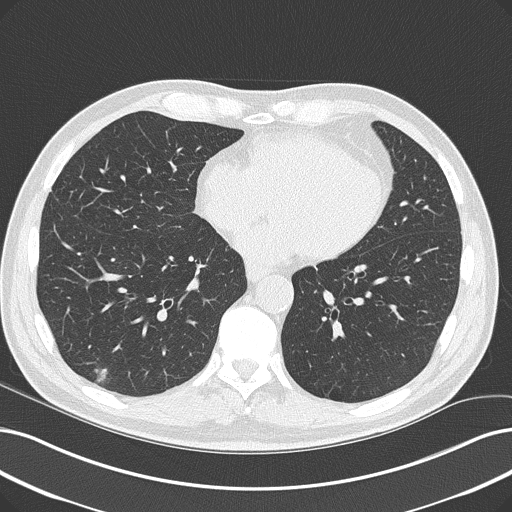
Low-dose screening chest CT, one axial slice. Slice 89 of 228 in the series (ordered by position). Reconstruction kernel B50f. Lung window (W 1500 / L -600 HU). 2 mm slice thickness. 512 × 512 image matrix, field of view 366 × 366 mm.
Outlined on this slice (expert manual segmentation):
- lesion 1 (tumor, lower lobe of right lung): bounding box [x1, y1, x2, y2] px = [94, 368, 107, 382]